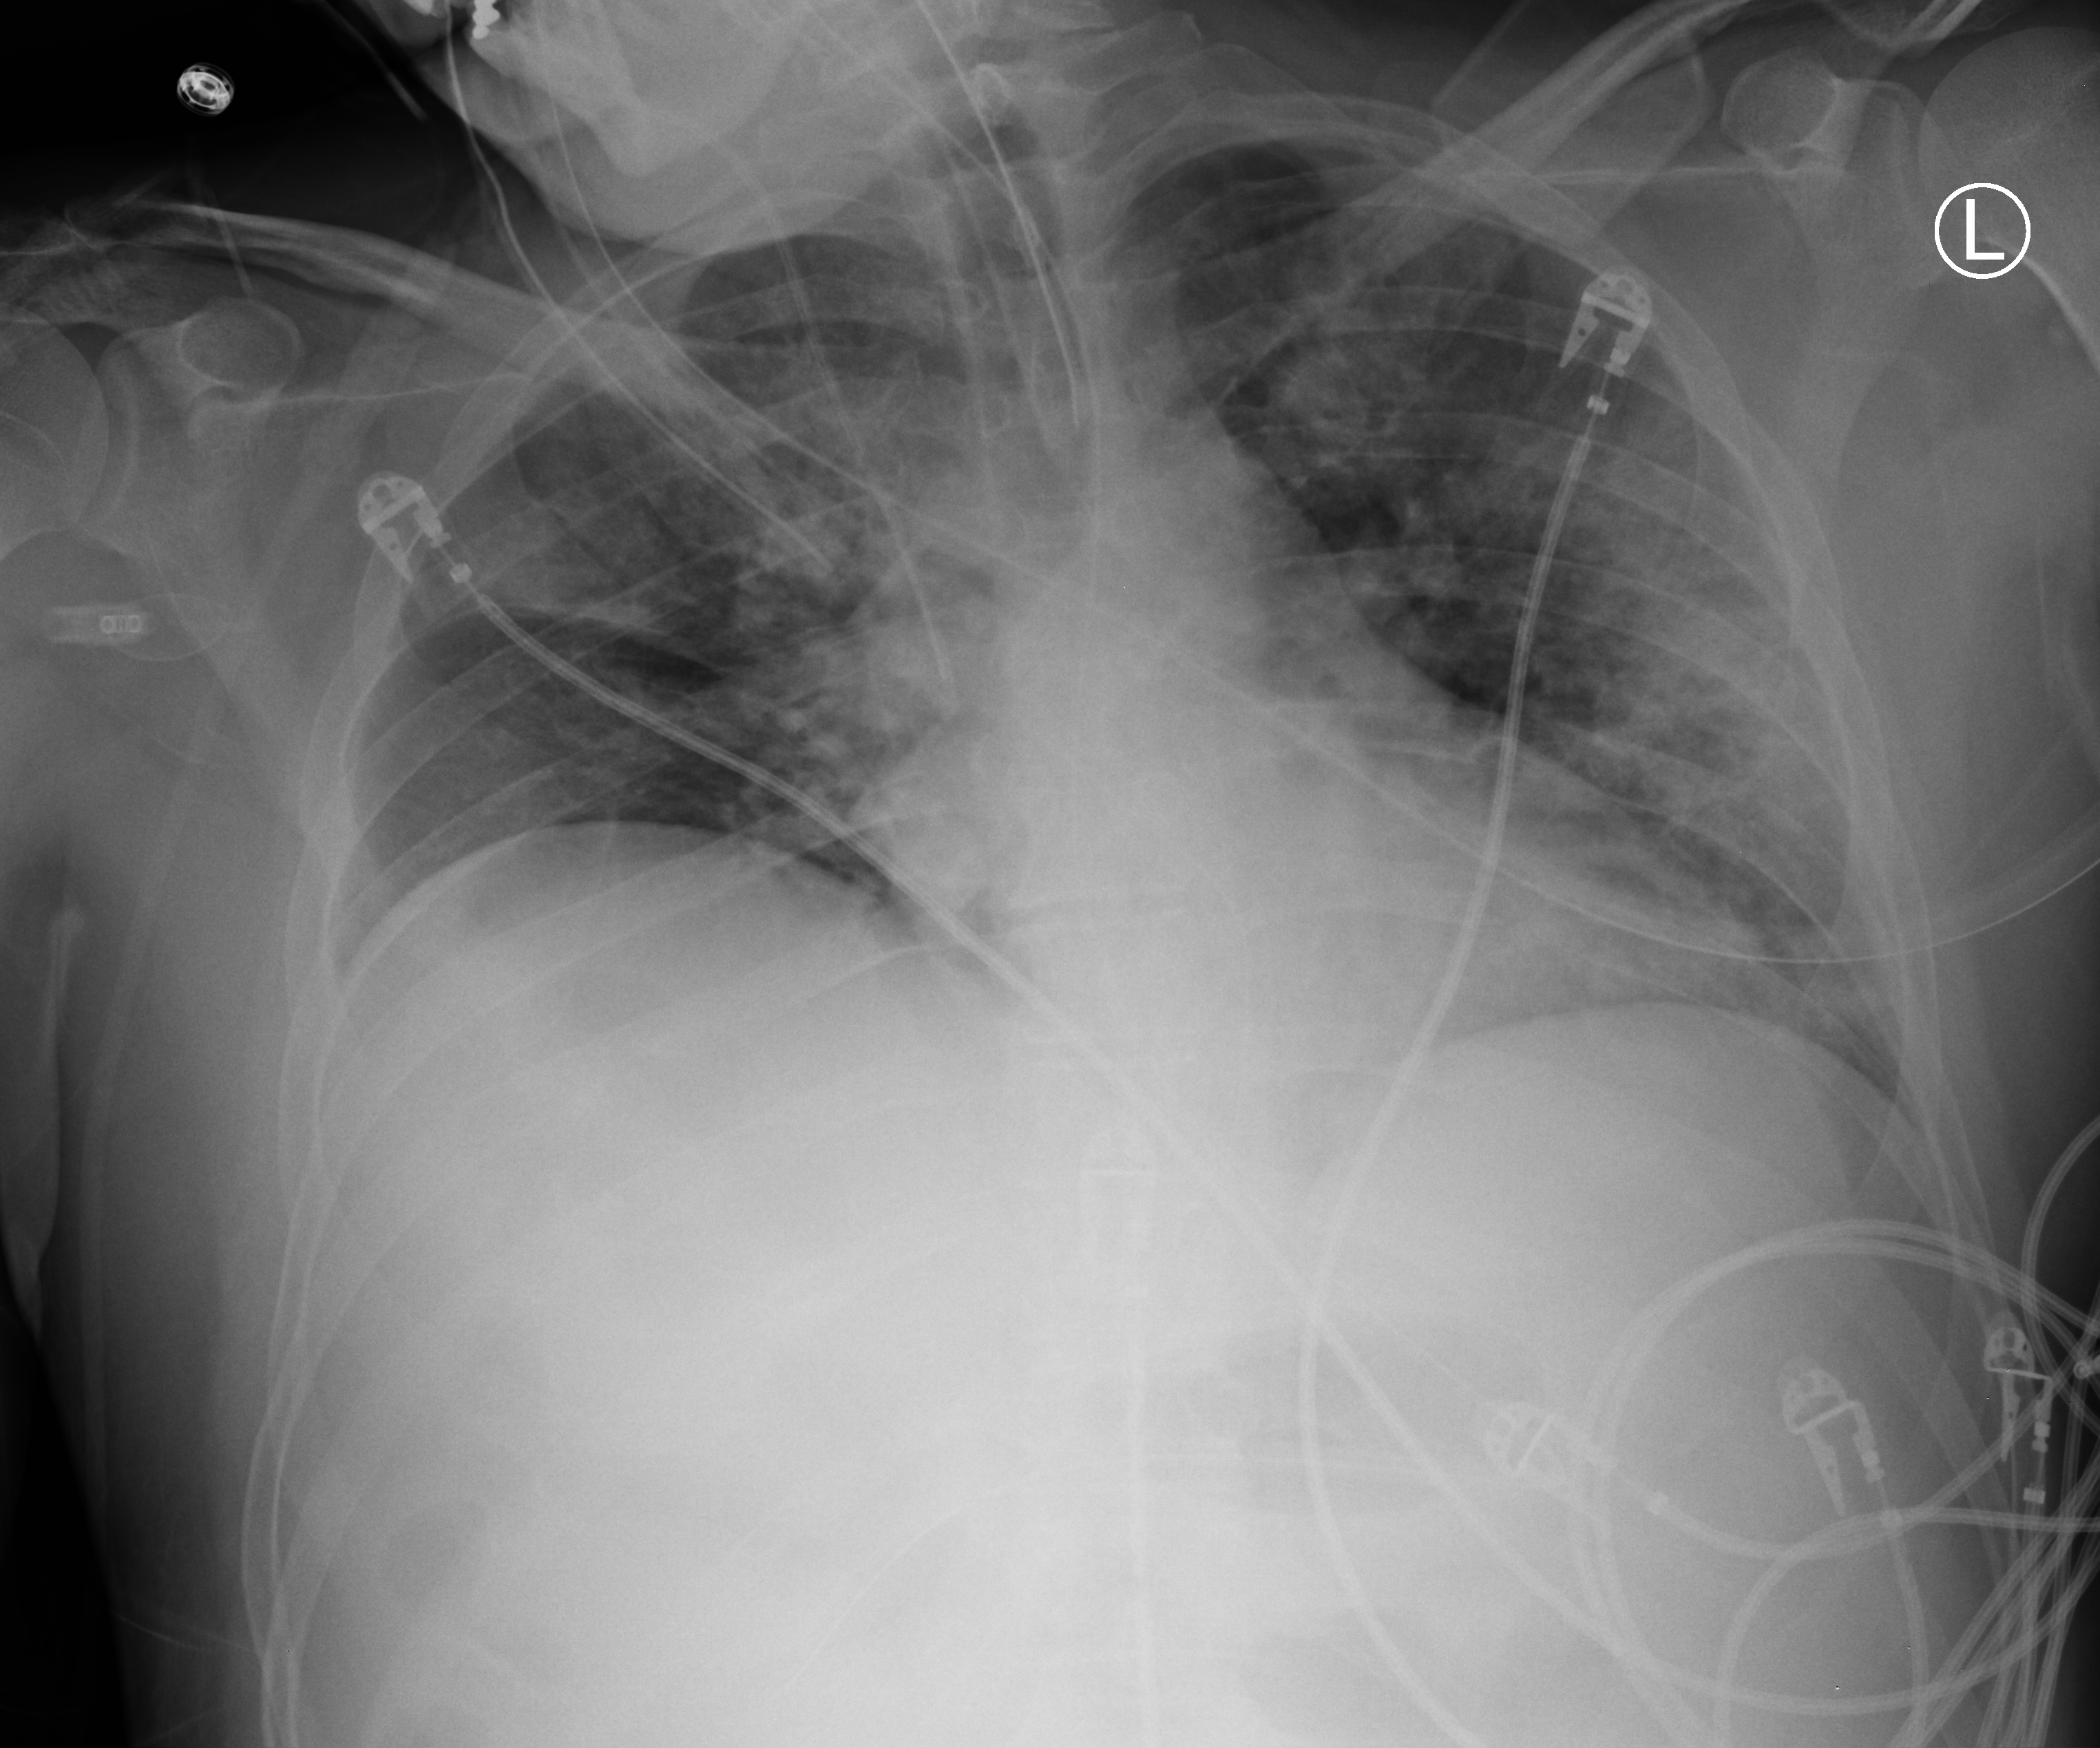
Chest X-ray (portable); anteroposterior (AP) projection. Male patient hospitalised with COVID-19, age 18–59 years.
Hospital-stay facts (about this admission, not read from this image; timing relative to this image not recorded): other chronic lung disease (admission record): no; mechanically ventilated during this hospital stay: yes; admitted to intensive care during this hospital stay: yes.